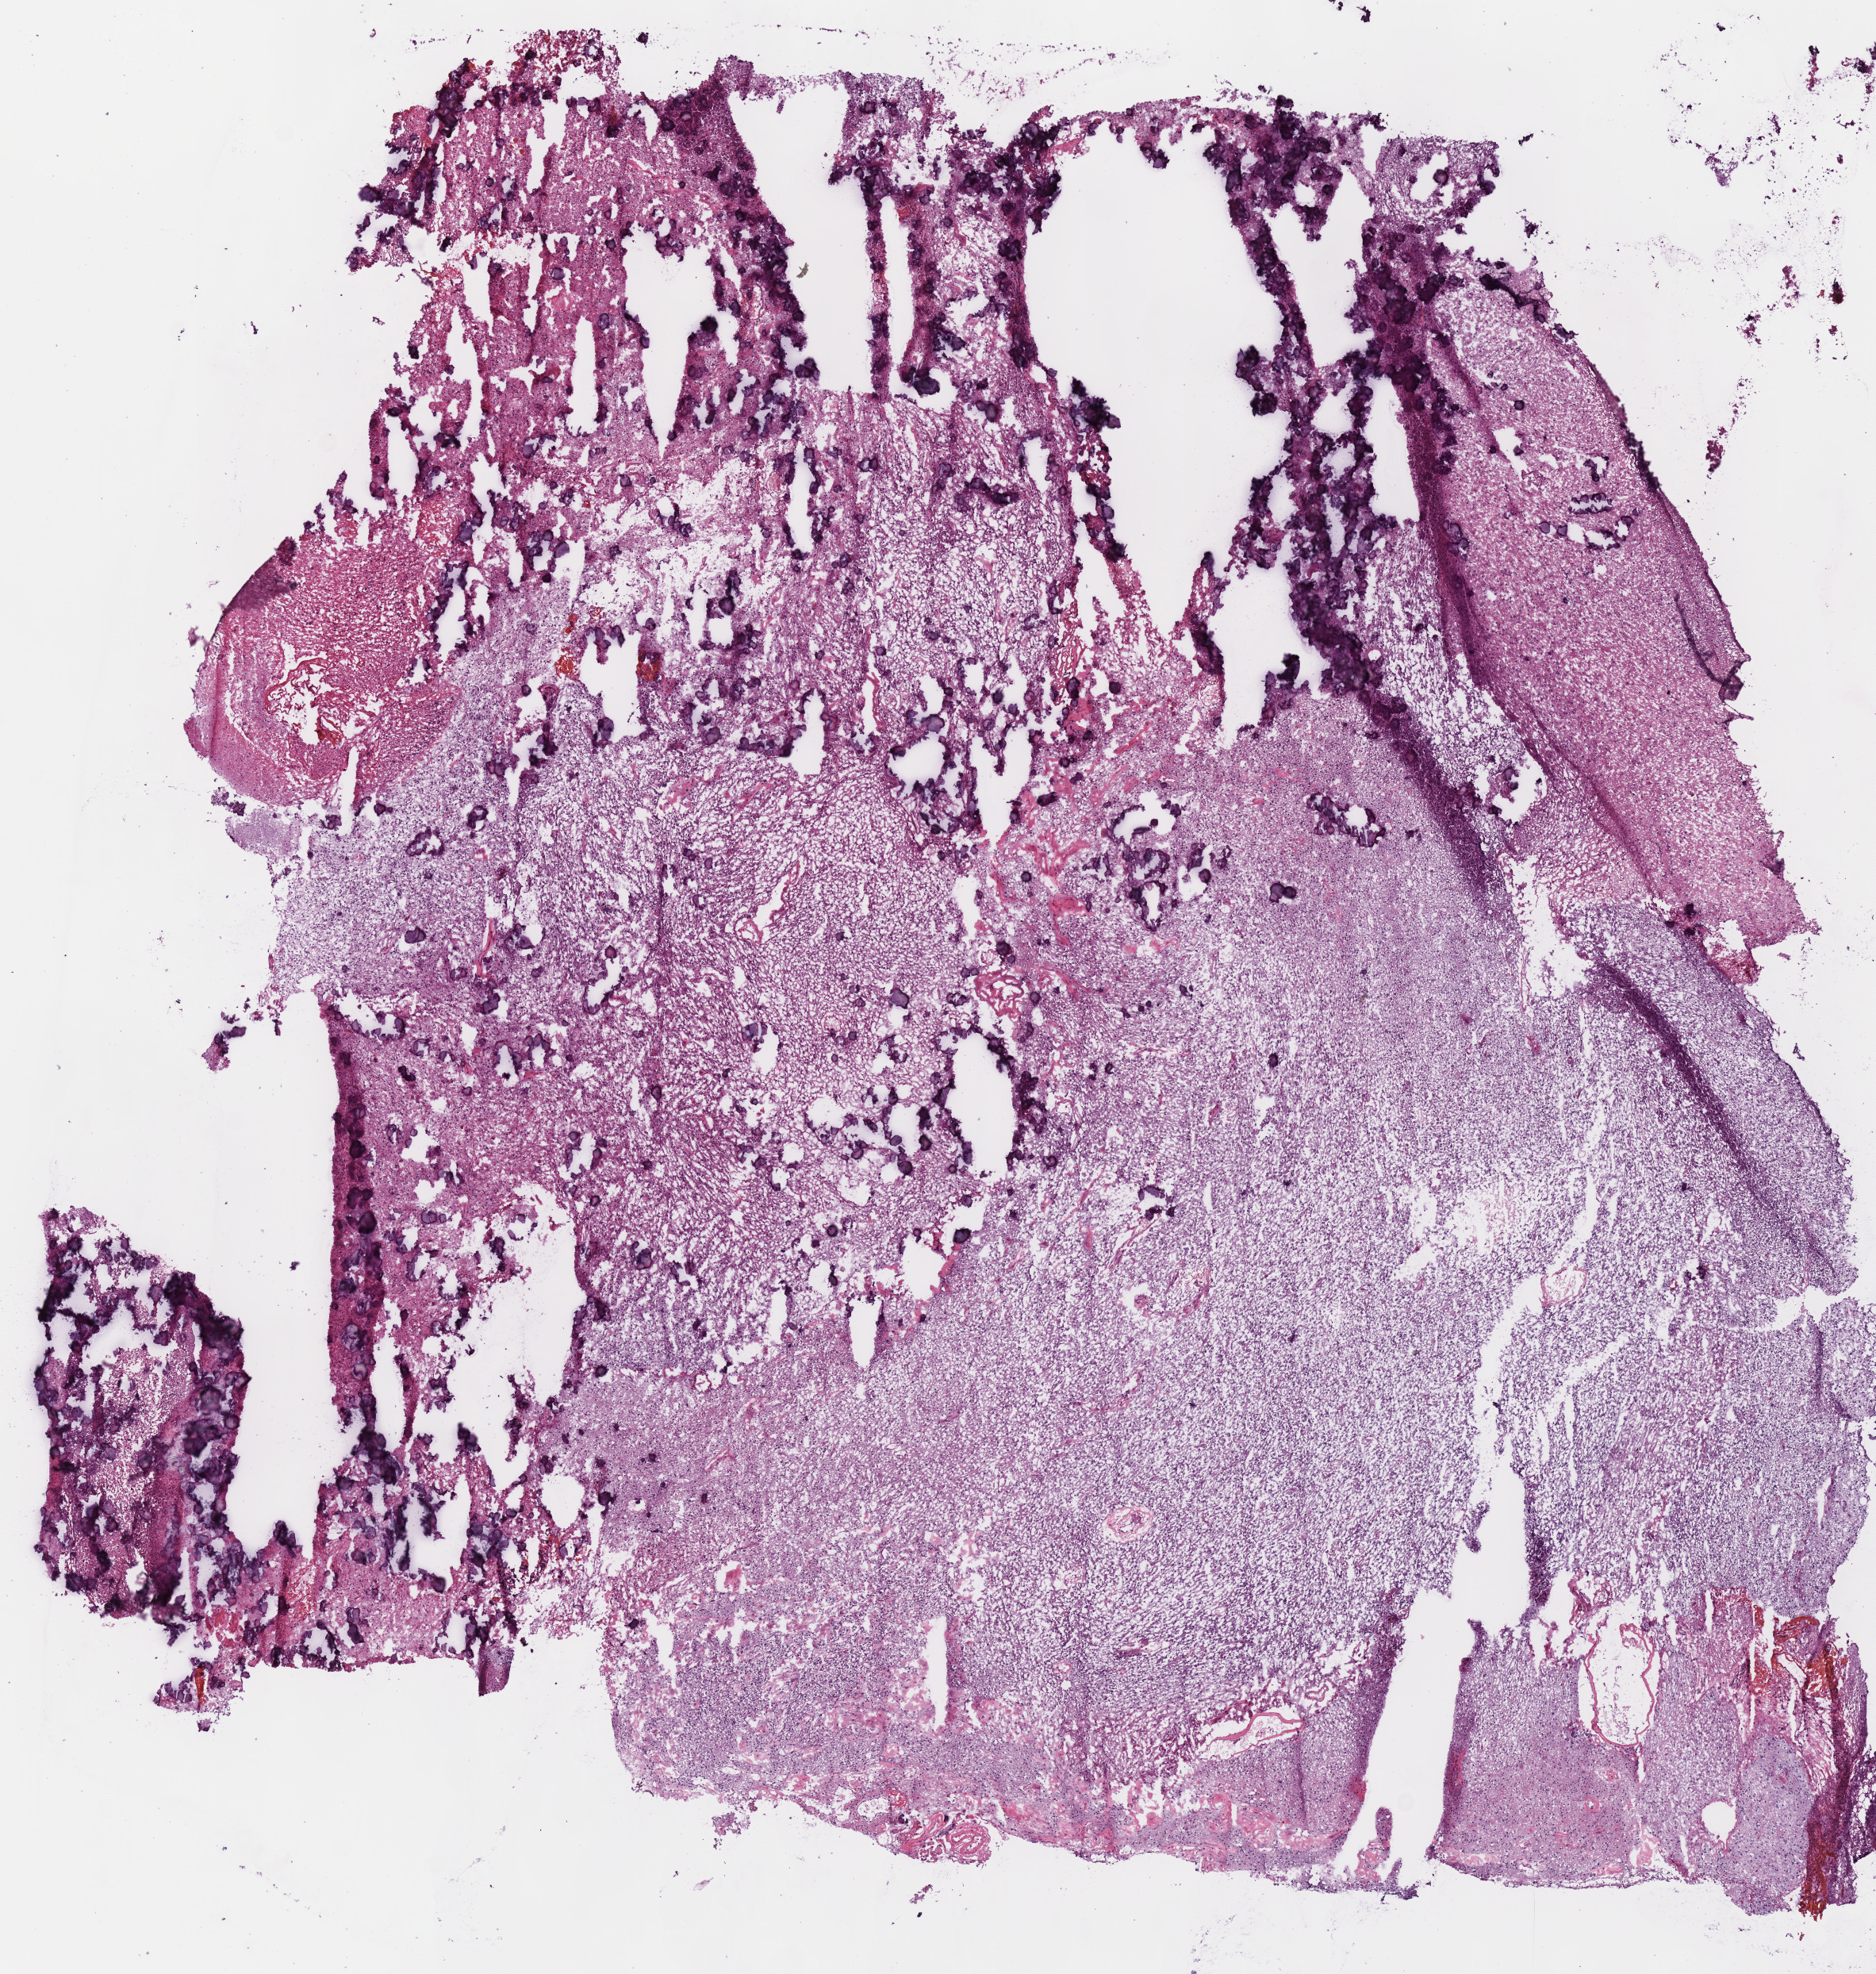
Whole-slide histology image, H&E — whole scanned area (about 9.3 x 9.8 mm) shown as a low-resolution overview, frozen section from the bottom of the tissue portion, brain, primary tumour sample. Patient: female, age at initial diagnosis 31 years. Slide review estimates, as recorded: tumour cells 100%, tumour nuclei 70%.
Pathologic diagnosis: Astrocytoma, NOS (cerebrum).